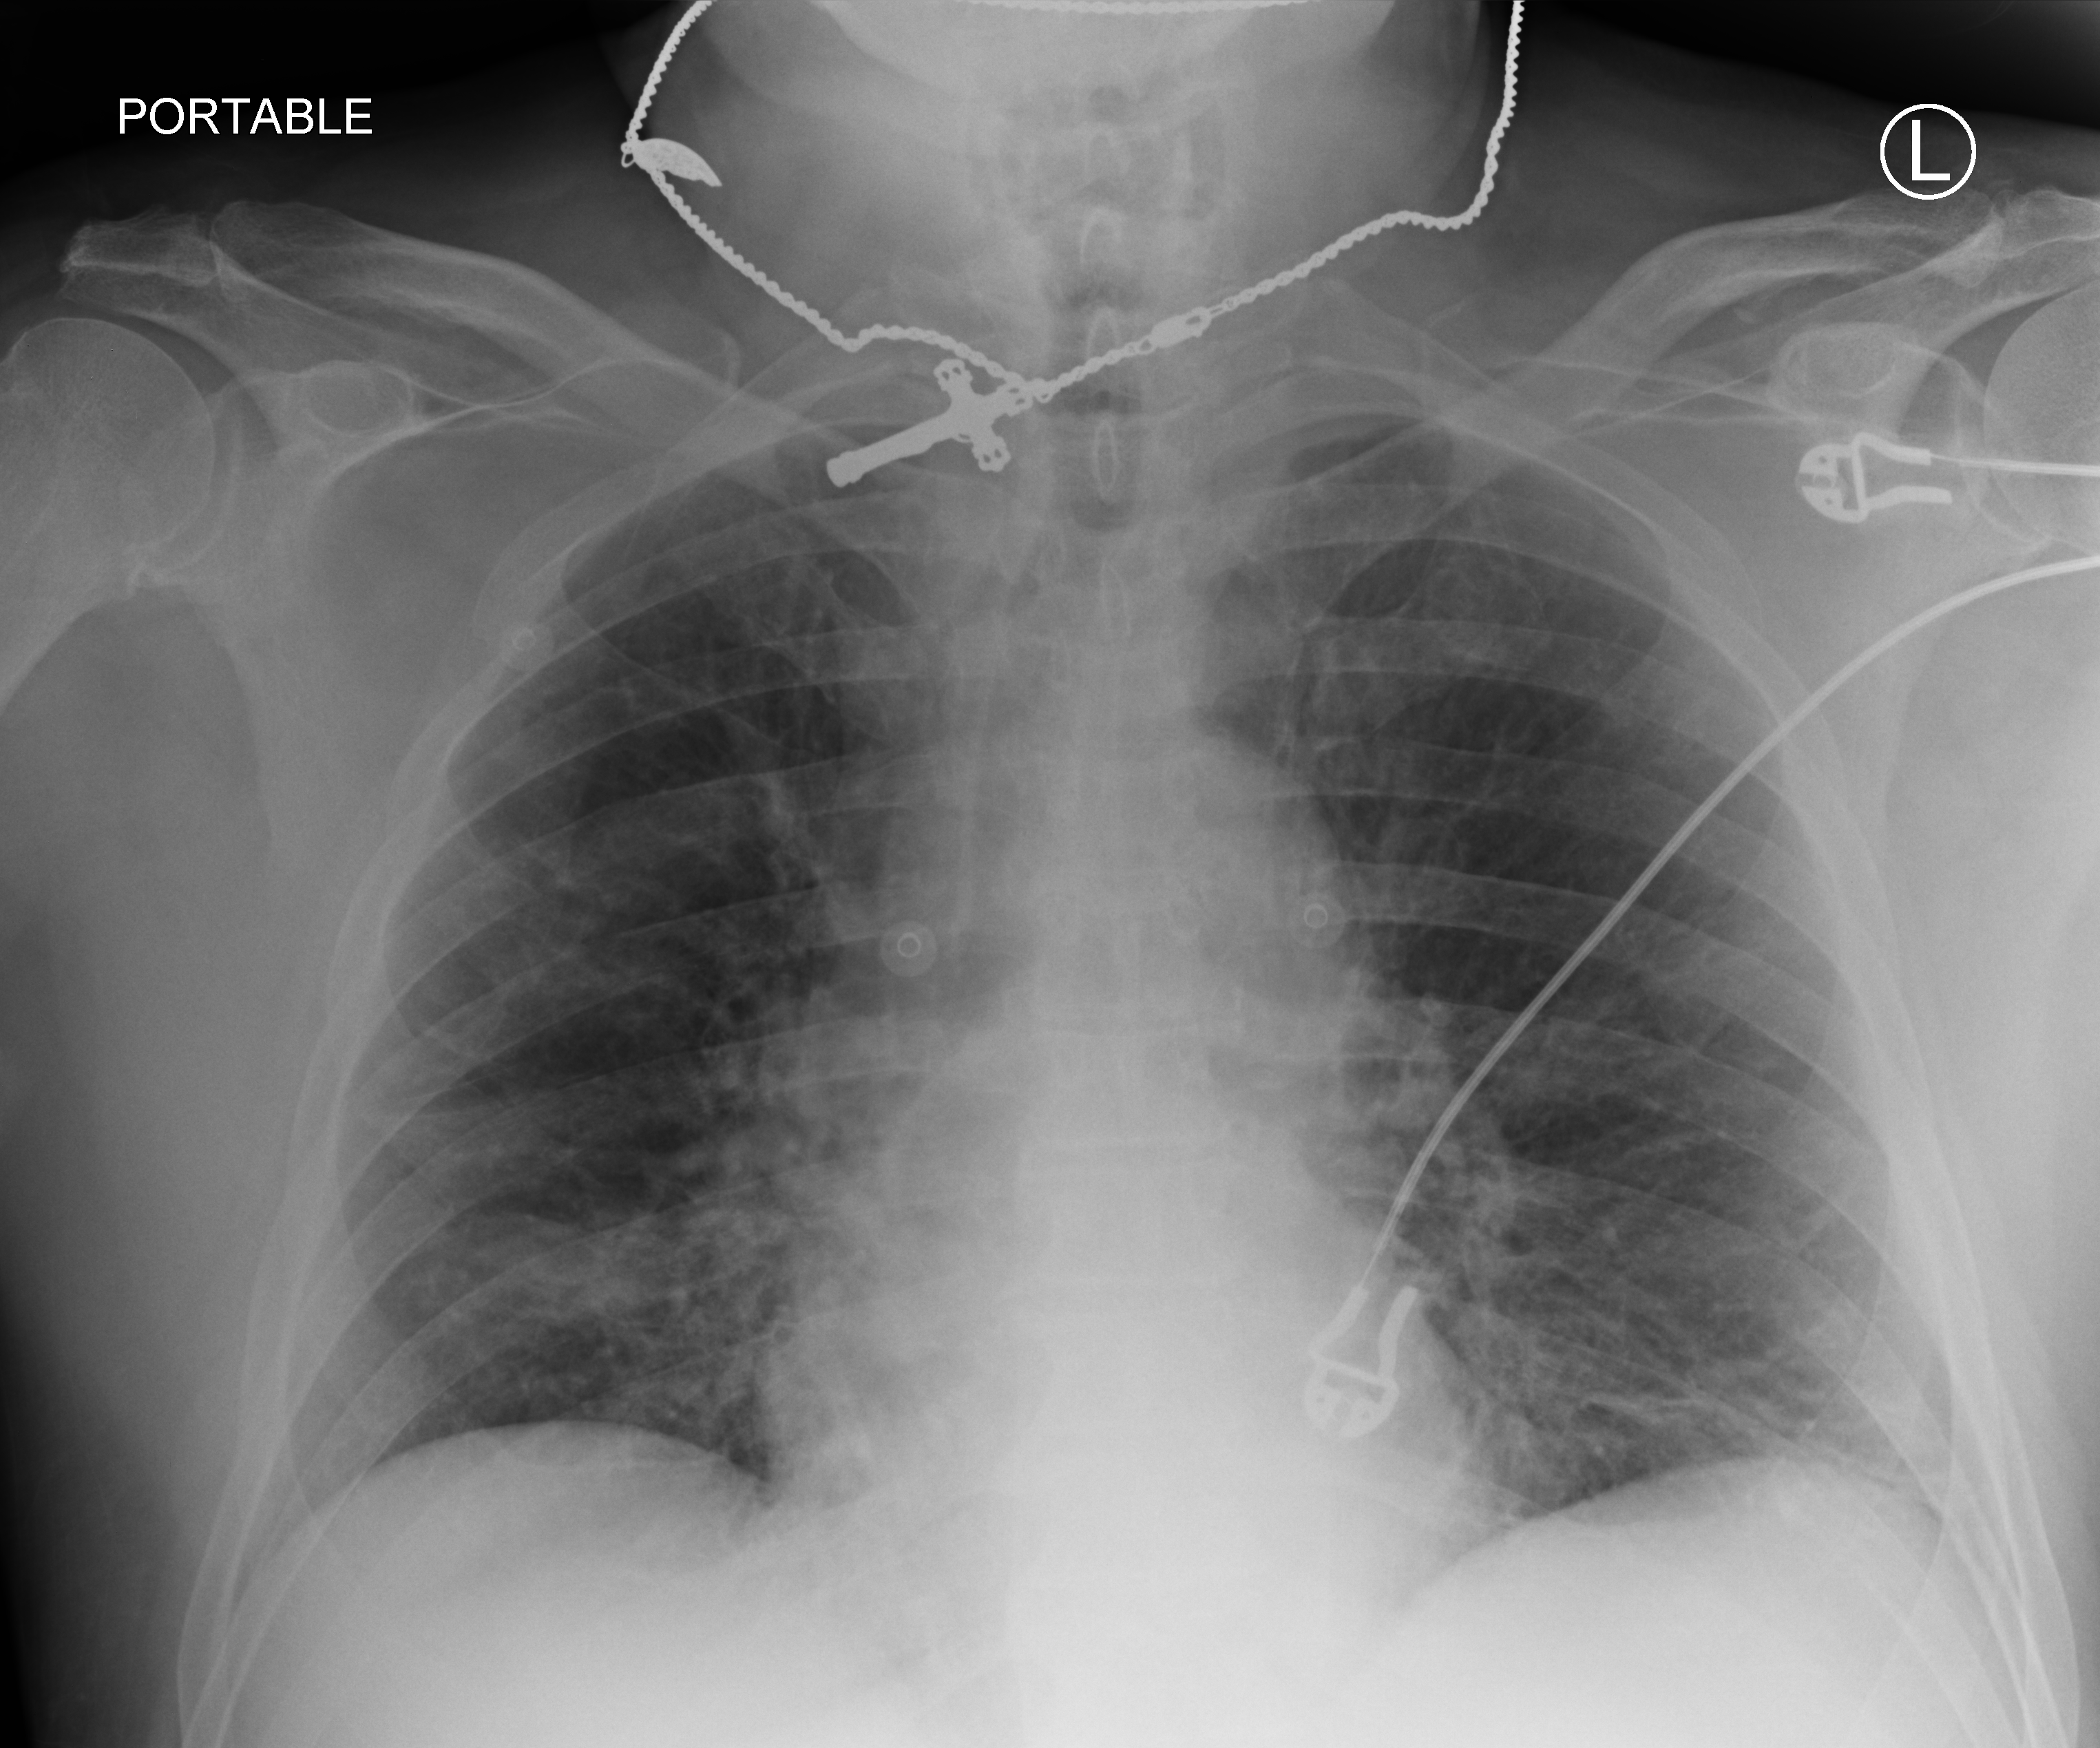
Bedside chest radiograph (computed radiography); anteroposterior (AP) projection. Male patient hospitalised with COVID-19, age 75–90 years.
Admission-level facts for this patient (not findings on this image; timing relative to this image not recorded):
- hypertension (admission record): yes